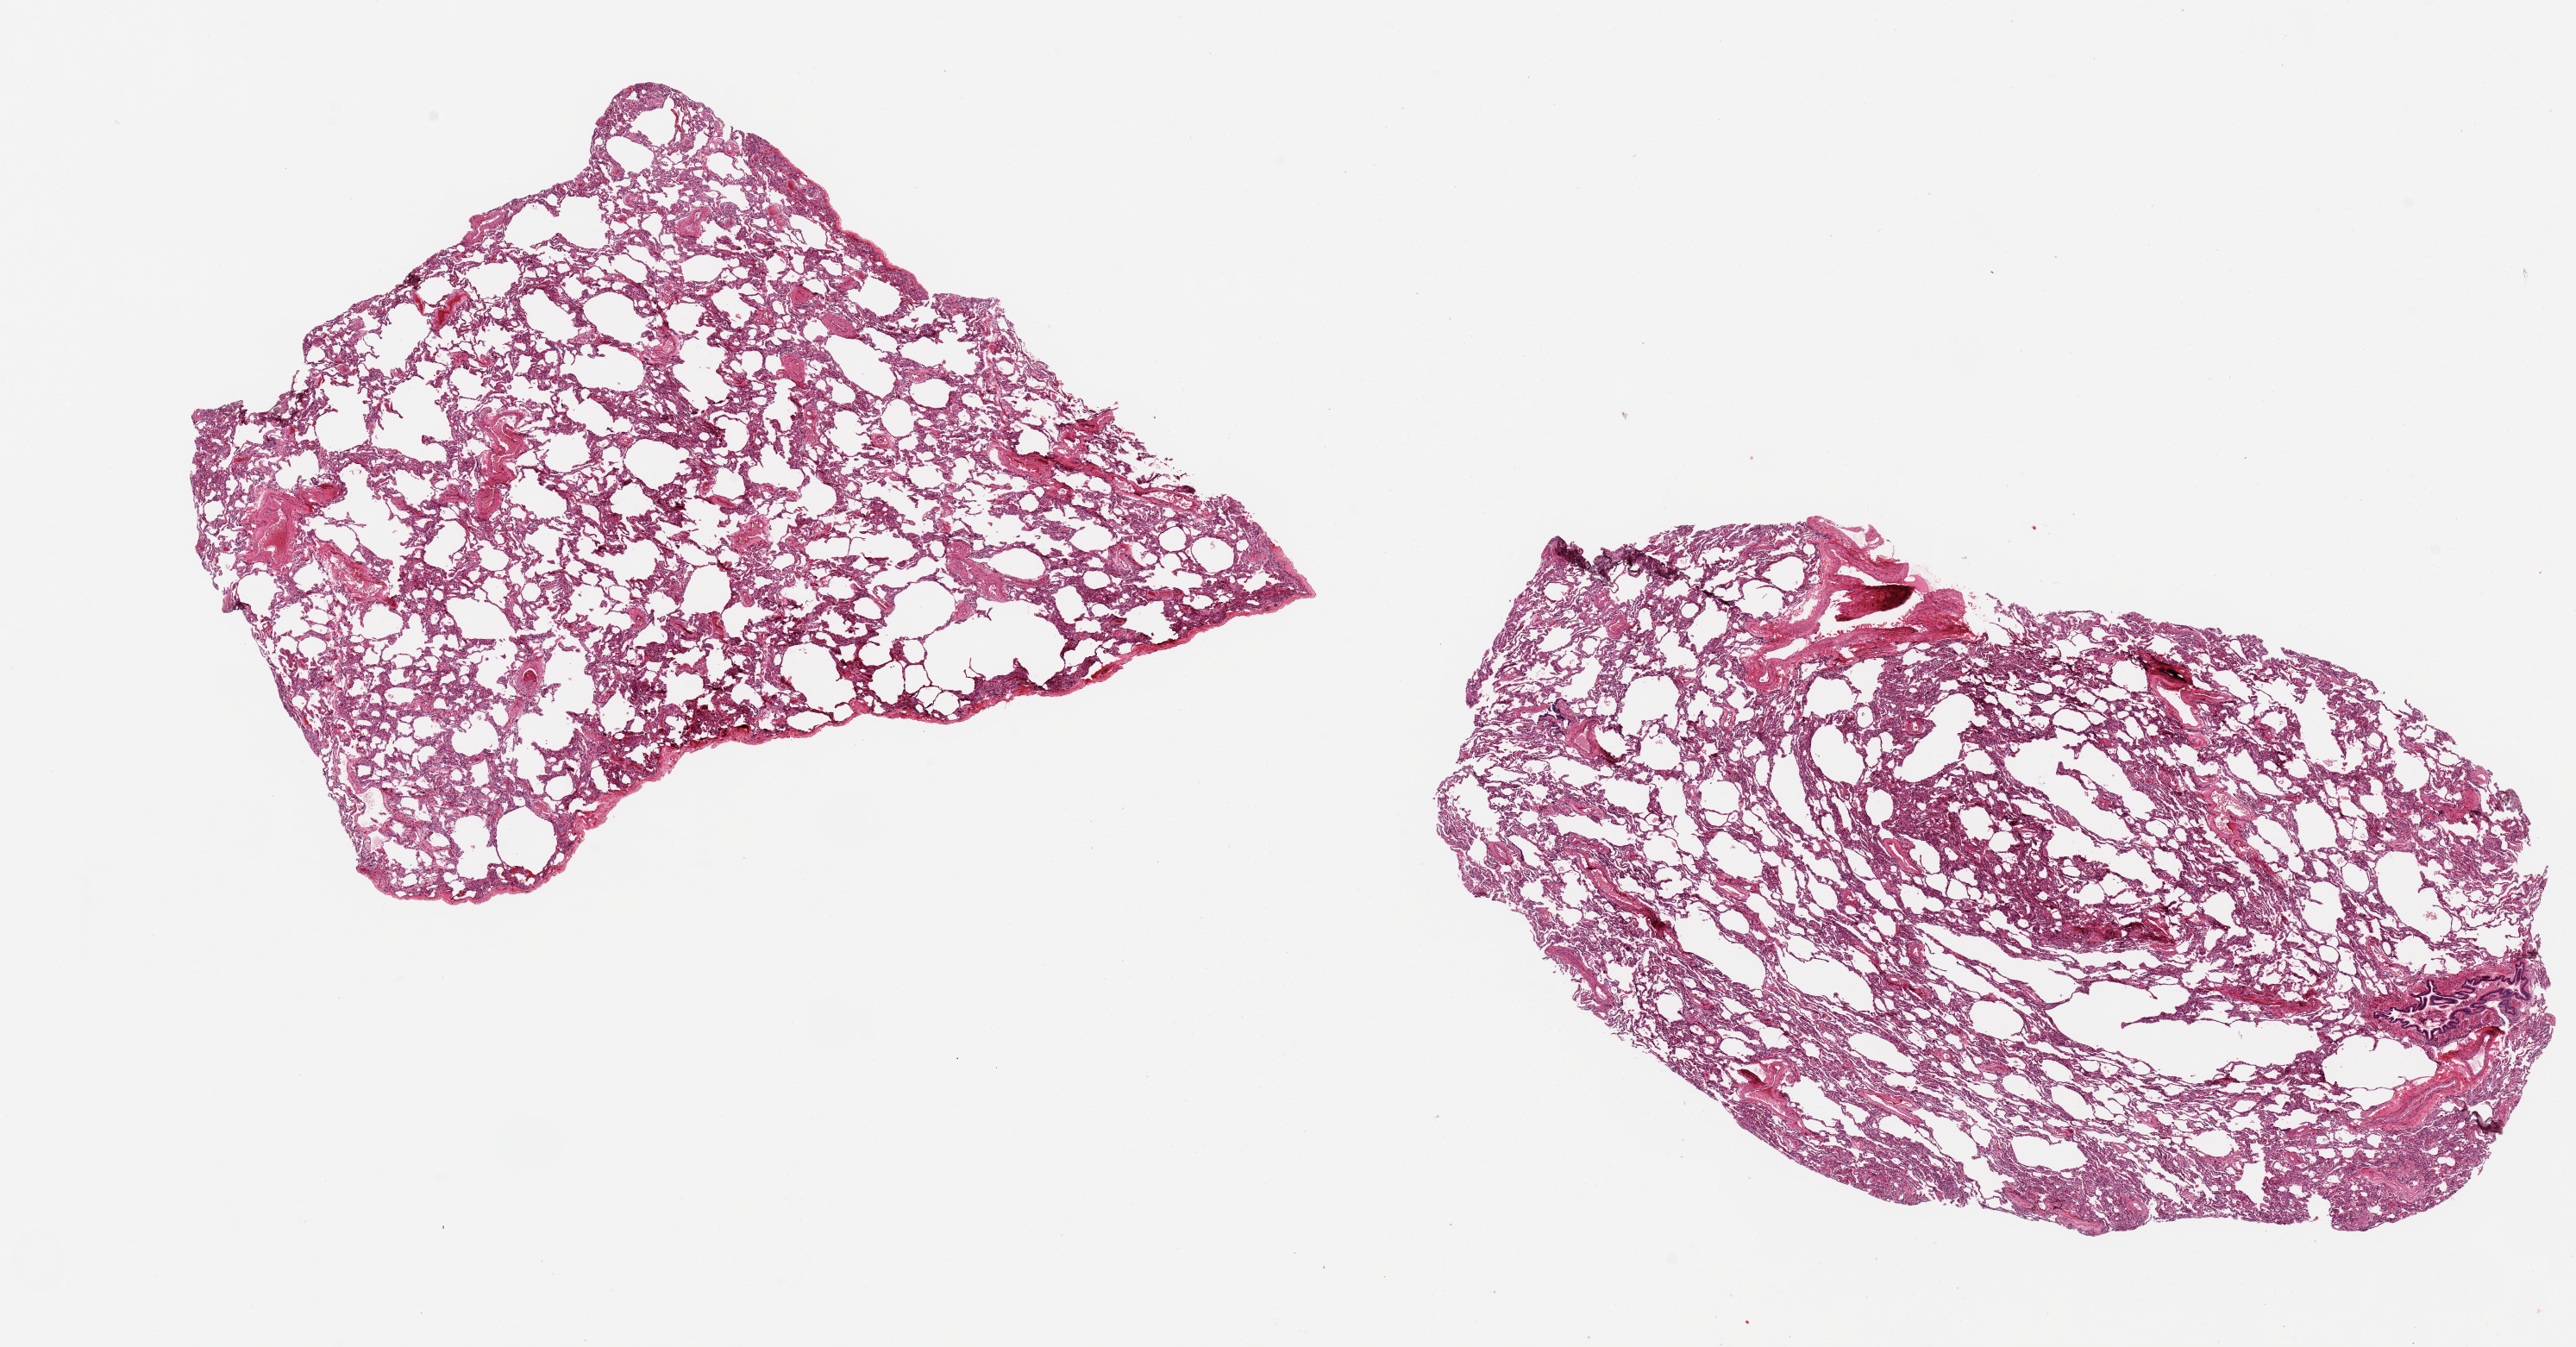
Haematoxylin and eosin whole-slide image — shown as a low-resolution overview of the whole scanned area (about 23.6 x 12.4 mm). PAXgene-fixed, paraffin-embedded tissue. Sampled site (target tissue): lung. Tissue donor sample. Donor sex: male.
* pathologist's review note for this sample: 2 aliquots, ~9x6mm. Minimal congestion/edema